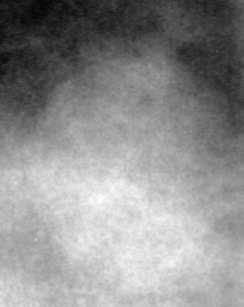
Cropped region of a digitized screen-film mammogram centred on a radiologist-marked abnormality; left breast; CC view.
Mass, shape round, margins obscured; BI-RADS assessment category 4; pathology (as recorded): benign.